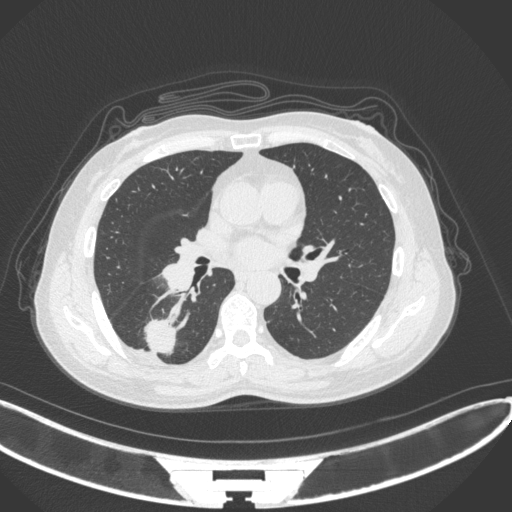
Chest CT, one axial slice. Position 160 of 352 along the scan axis. Reconstruction kernel B31f. Lung window (W 1500 / L -600 HU). 512 × 512 image matrix, field of view 400 × 400 mm. Female patient, age 55 years. From the clinical record (not read from this slice): clinical TNM (as recorded): T1c N1 M0.
Annotated regions visible in this slice (rectangle marked by the reading radiologist):
- lung tumour (recorded histology: adenocarcinoma): bounding box [x1, y1, x2, y2] px = [139, 317, 181, 357]